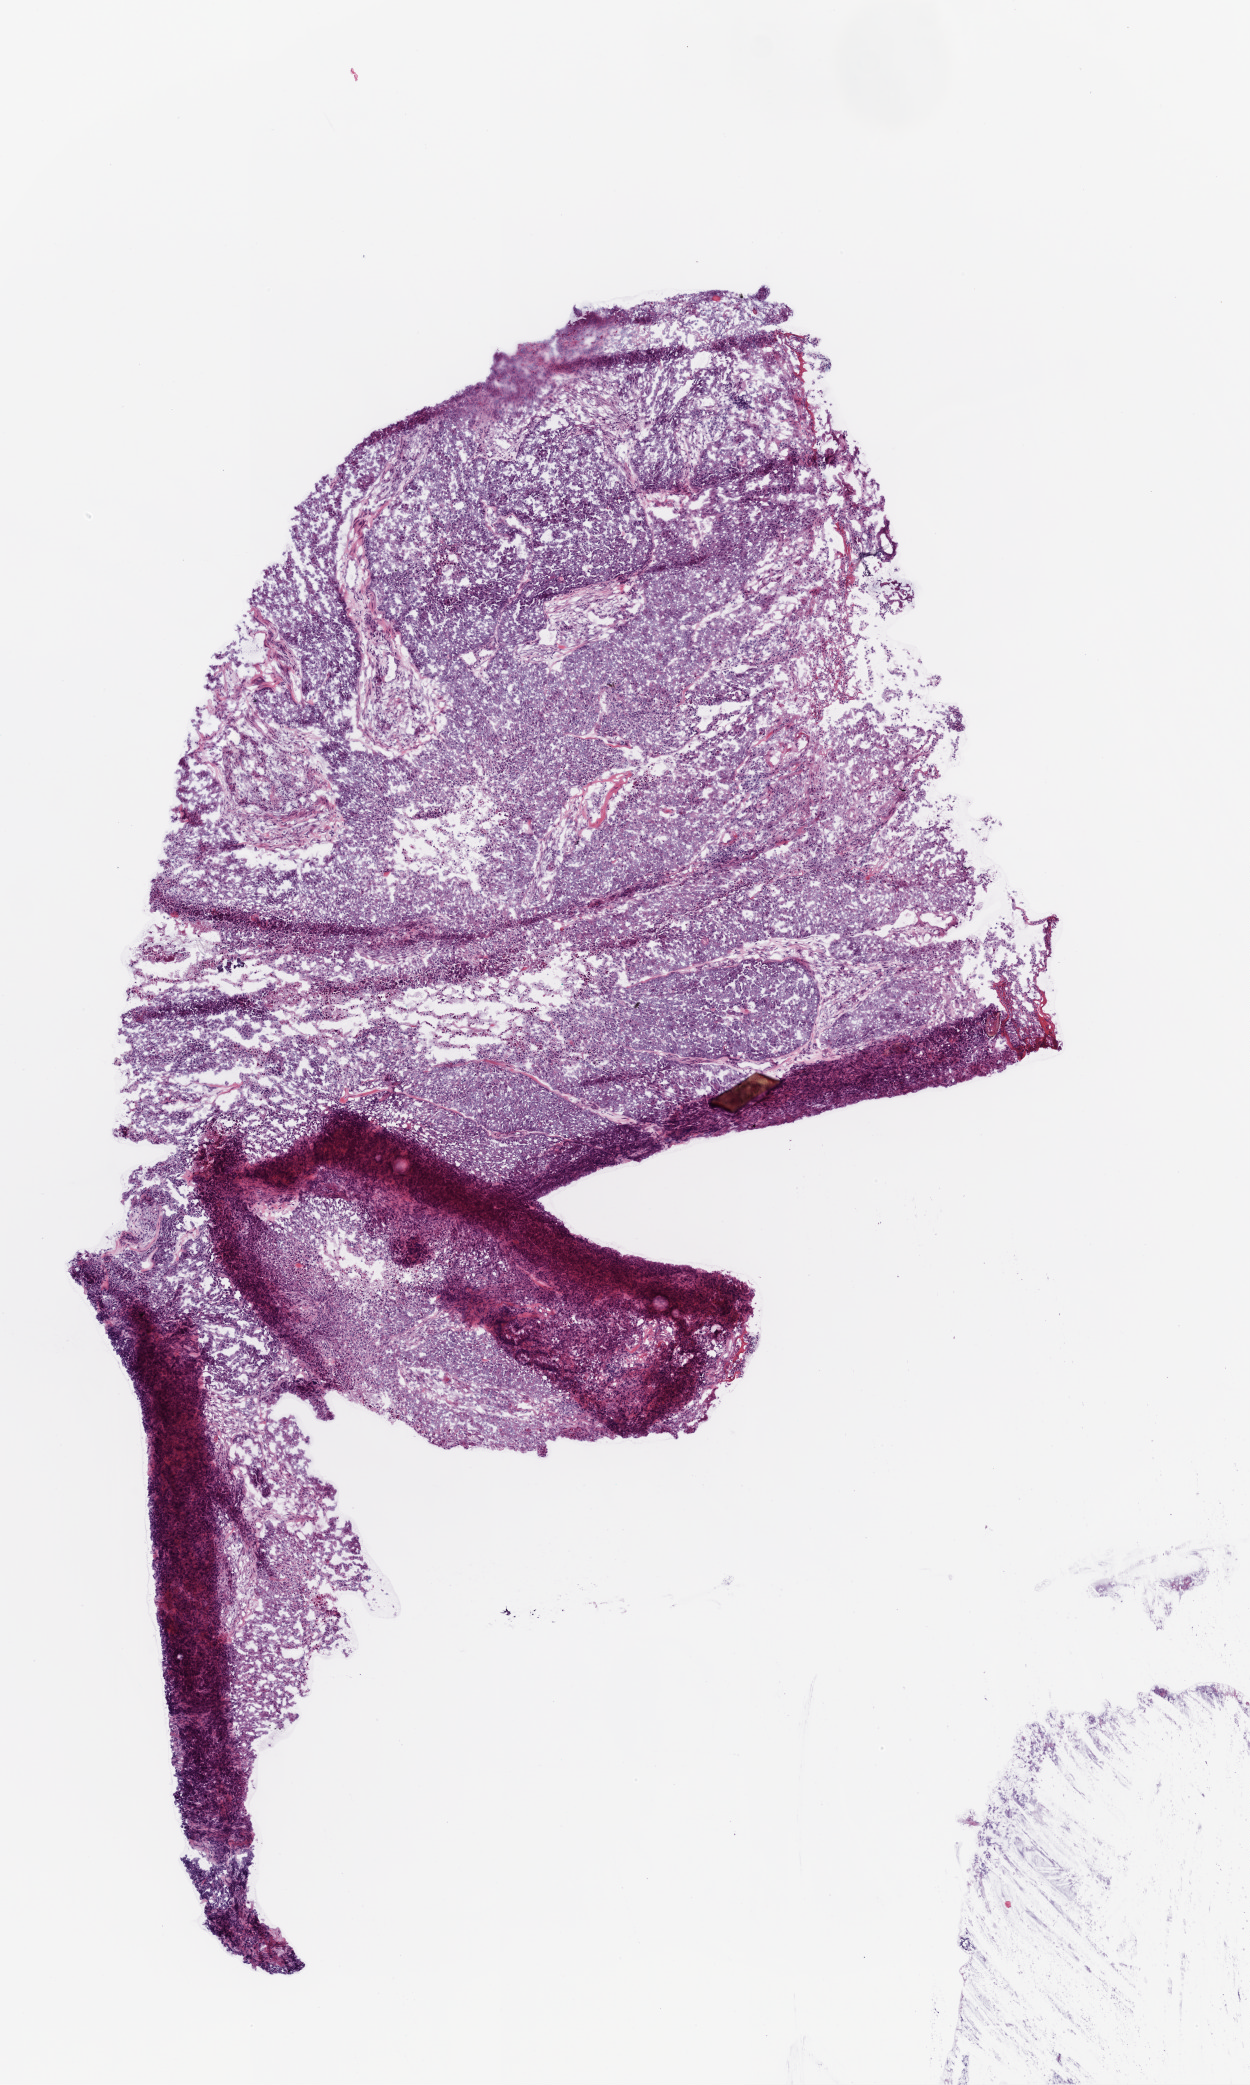
Digitized H&E tissue section (whole slide), shown as a low-resolution overview of the whole scanned area (about 5.0 x 8.4 mm). Frozen section. Ovary, primary tumour sample. Patient: female, age at initial diagnosis 65 years. Histologic grade: G3 (poorly differentiated). Slide review estimates, as recorded: tumour cells 94%, tumour nuclei 95%, normal cells 0%, stromal cells 5%, necrosis 1%.
Laterality: right. FIGO stage: IIIC. Diagnosis: Serous cystadenocarcinoma, NOS.